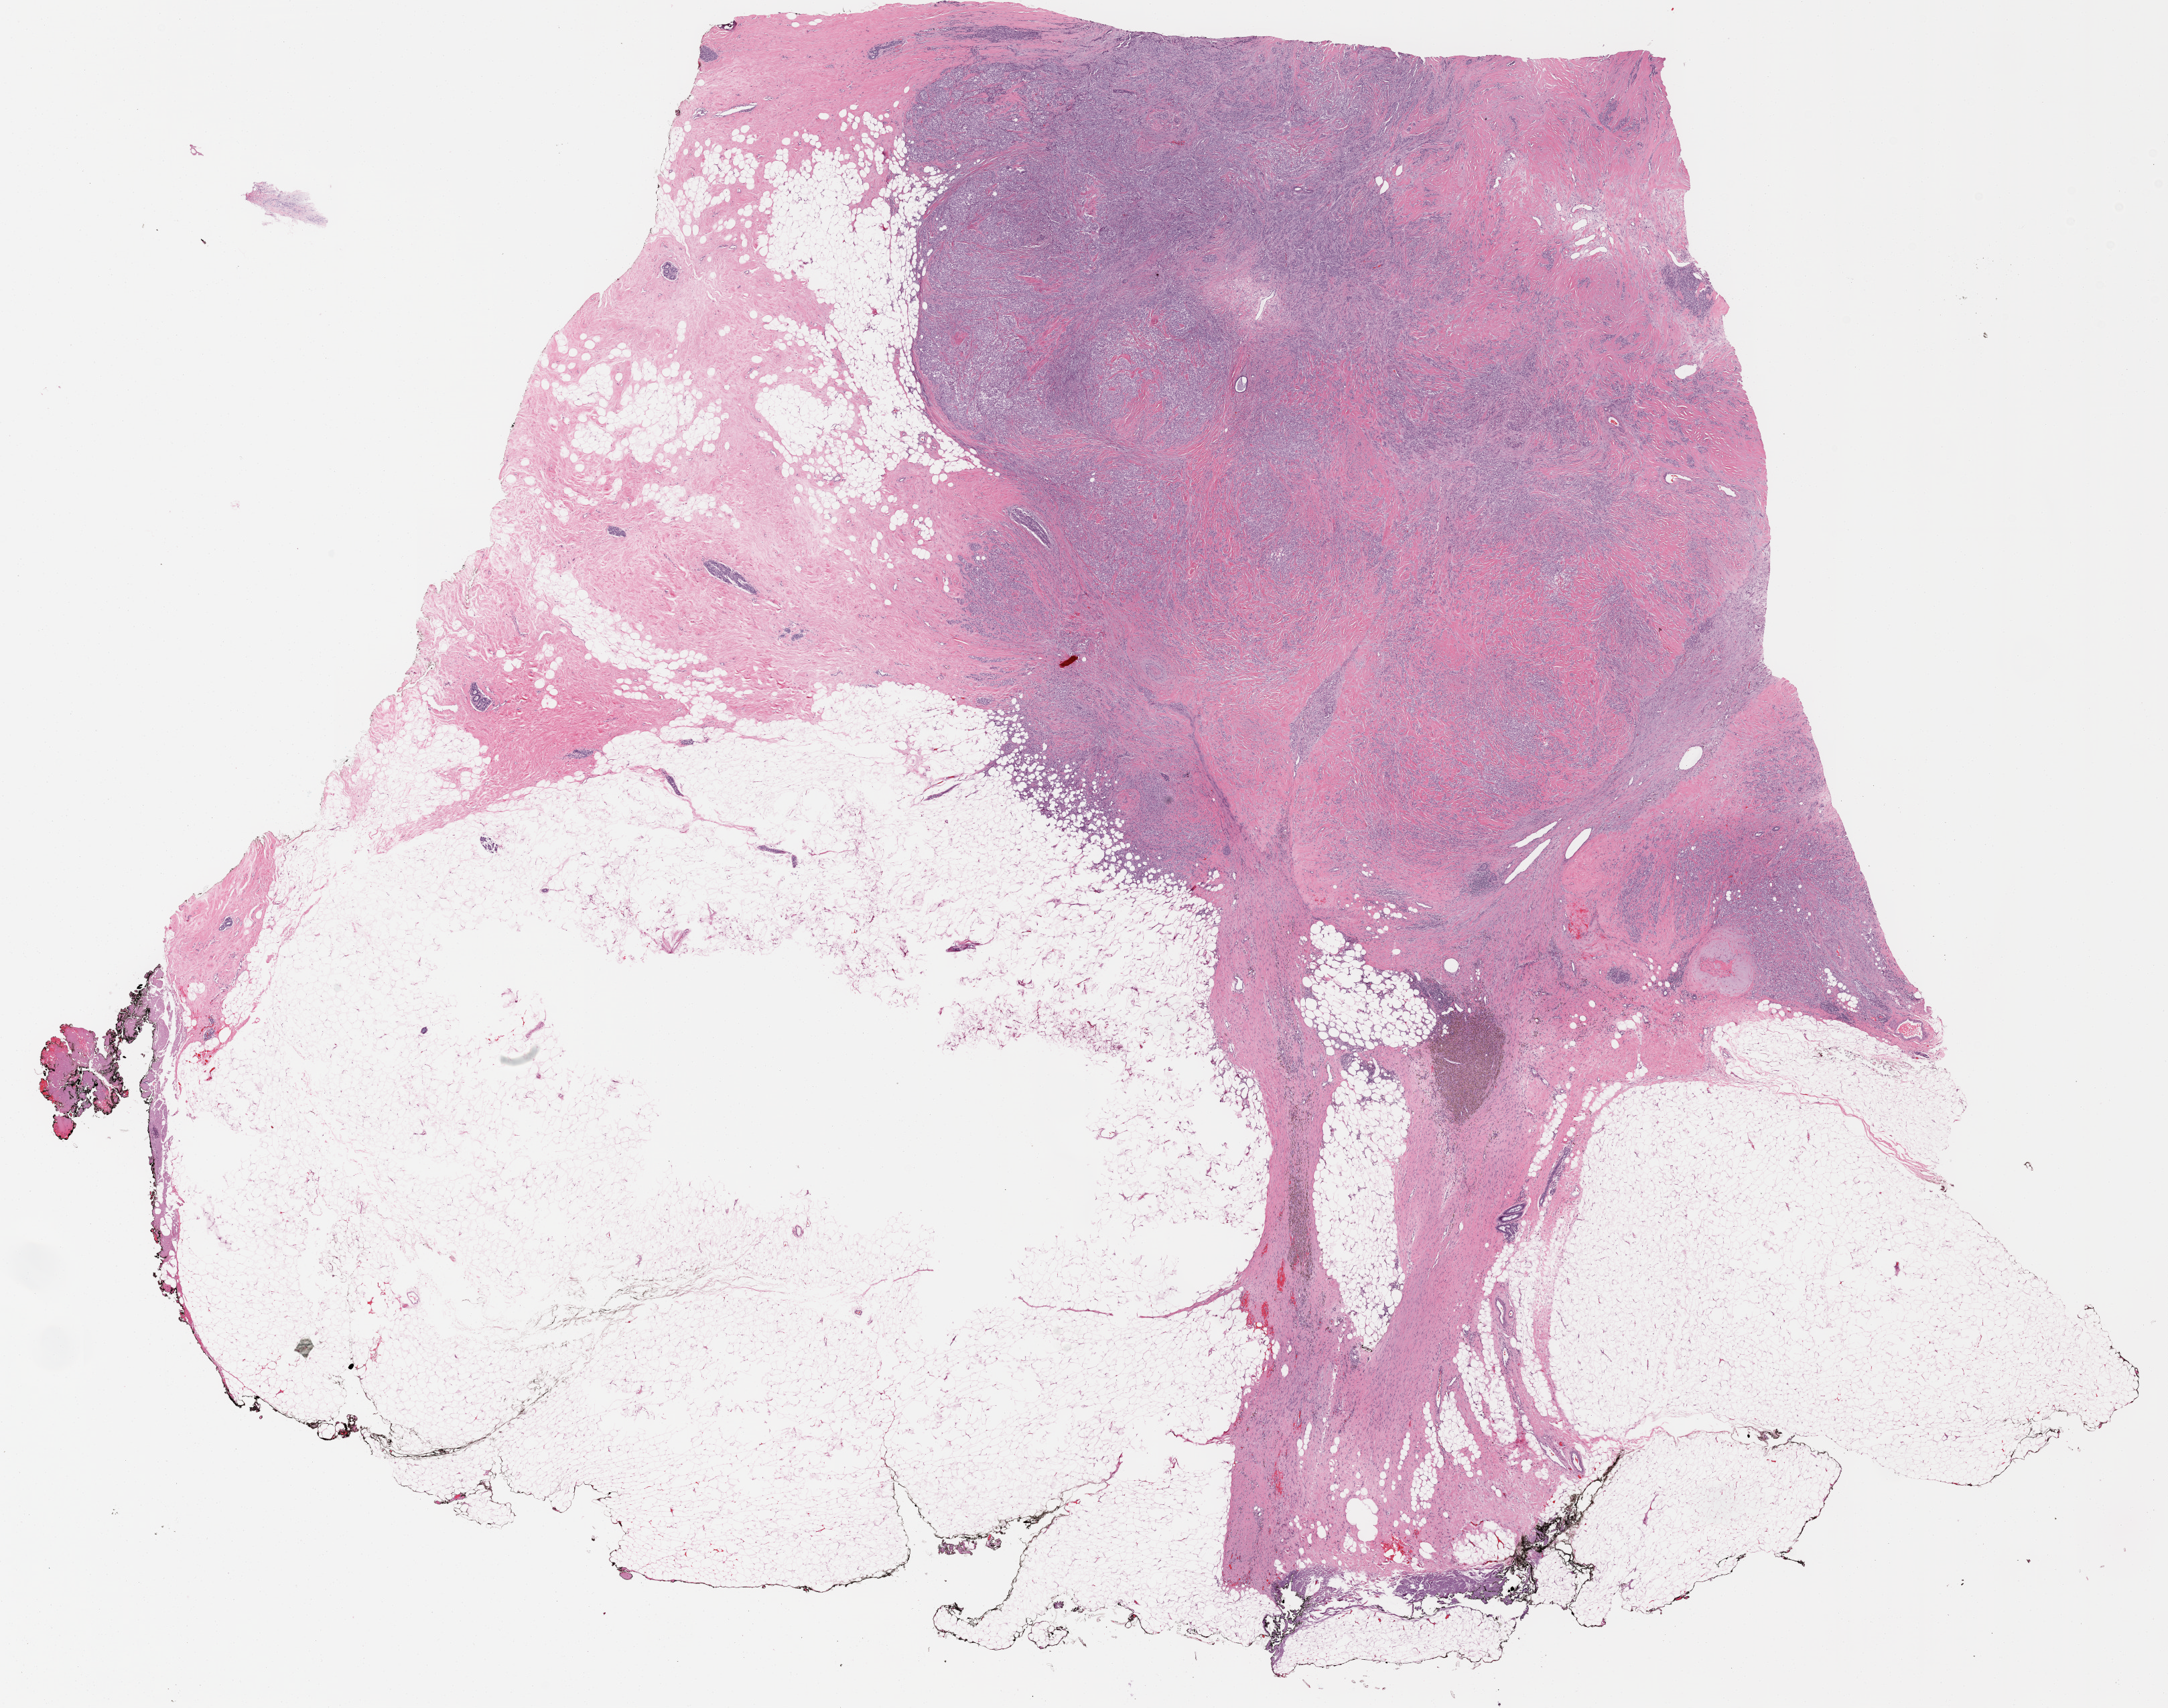
Digitized H&E-stained tissue section (whole slide) — whole scanned area (about 25.9 x 20.4 mm, from a 20x scan) shown as a low-resolution overview, formalin-fixed paraffin-embedded (FFPE) diagnostic section, sample: primary tumour, breast. Patient: female, age at initial diagnosis 61 years.
TNM: T2 N0 (i+) M0. AJCC pathologic stage: IIA. Pathologic diagnosis: Lobular carcinoma, NOS. Lymph nodes positive (case pathology): 0 of 2 examined.